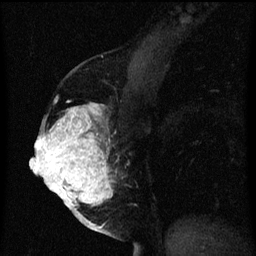
Breast MRI (dynamic contrast-enhanced), one sagittal slice; position 30 of 60 along the scan axis; dynamic contrast-enhanced series, image 2 of 3 at this slice position (ordered by acquisition); 1.5 T; TE 4.2 ms, TR 8 ms; 2 mm slice thickness; 256 × 256 image matrix. Female patient, age 56 years.
Outlined on this slice (semi-automatic segmentation, software-assisted and operator-edited):
- analysis volume of interest (the breast-tissue region the enhancement analysis was run in; not a lesion): box from (x=40, y=104) to (x=121, y=209) px
- tumour enhancement mask (voxels above the 70 % enhancement threshold inside the analysis volume of interest): (x=40, y=104)–(x=113, y=209)